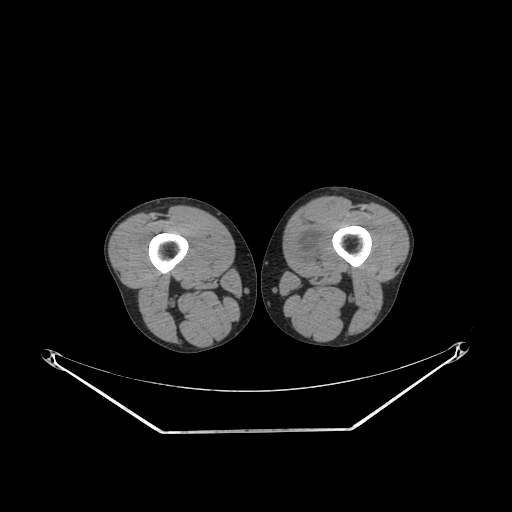
CT of an extremity soft-tissue mass (from a PET/CT study), one axial slice; slice 229 of 311 in the series (ordered by position); reconstruction kernel SOFT; 140 kVp; soft-tissue window (W 400 / L 40 HU); 512 × 512 image matrix, field of view 500 × 500 mm. Male patient. Case-level facts recorded for this patient, not image findings: histological type: mixoid liposarcoma; grade: low; site of the primary tumour: left thigh.
Outlined on this slice (expert contour drawn on MRI and transferred to this co-registered scan by the dataset authors):
- gross tumour volume (mass): box from (x=294, y=231) to (x=318, y=257) px